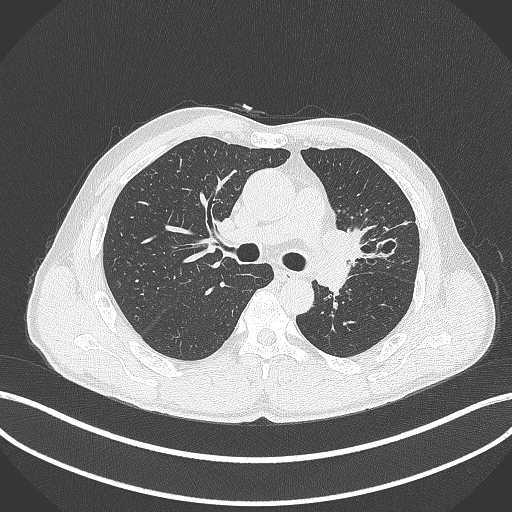
Chest CT, one axial slice. Slice 260 of 429 in the series (ordered by position). Reconstruction kernel B70f. Lung window (W 1500 / L -600 HU). 1 mm slice thickness. 512 × 512 image matrix, field of view 400 × 400 mm. Male patient, age 57 years. Case-level facts recorded for this patient, not image findings: clinical TNM (as recorded): T2b N0 M0.
Outlined on this slice (bounding box drawn by a radiologist):
- lung tumour (recorded histology: squamous cell carcinoma): bounding box (x1, y1, x2, y2) in pixels: (315, 224, 373, 270)